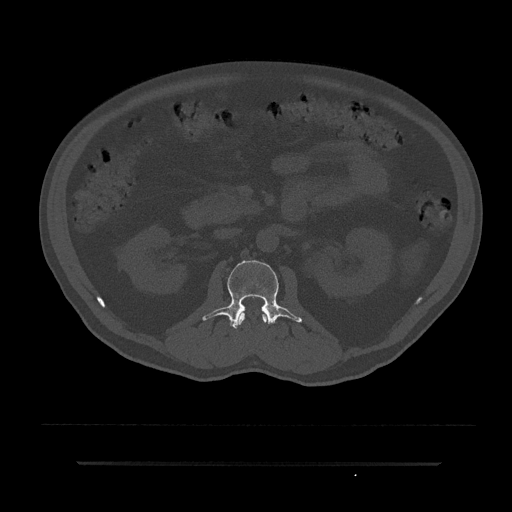
CT including the spine, one axial slice. Position 88 of 797 along the scan axis. 120 kVp. Bone window (W 1800 / L 400 HU). 512 × 512 image matrix. Male patient, age 59 years. From the clinical record (not read from this slice): primary cancer: bile ducts.
Structures marked on this image (semi-automatic segmentation, software-assisted and operator-edited):
- L1 vertebra: box from (x=237, y=311) to (x=268, y=325) px
- L2 vertebra: (x=202, y=260)–(x=302, y=329)